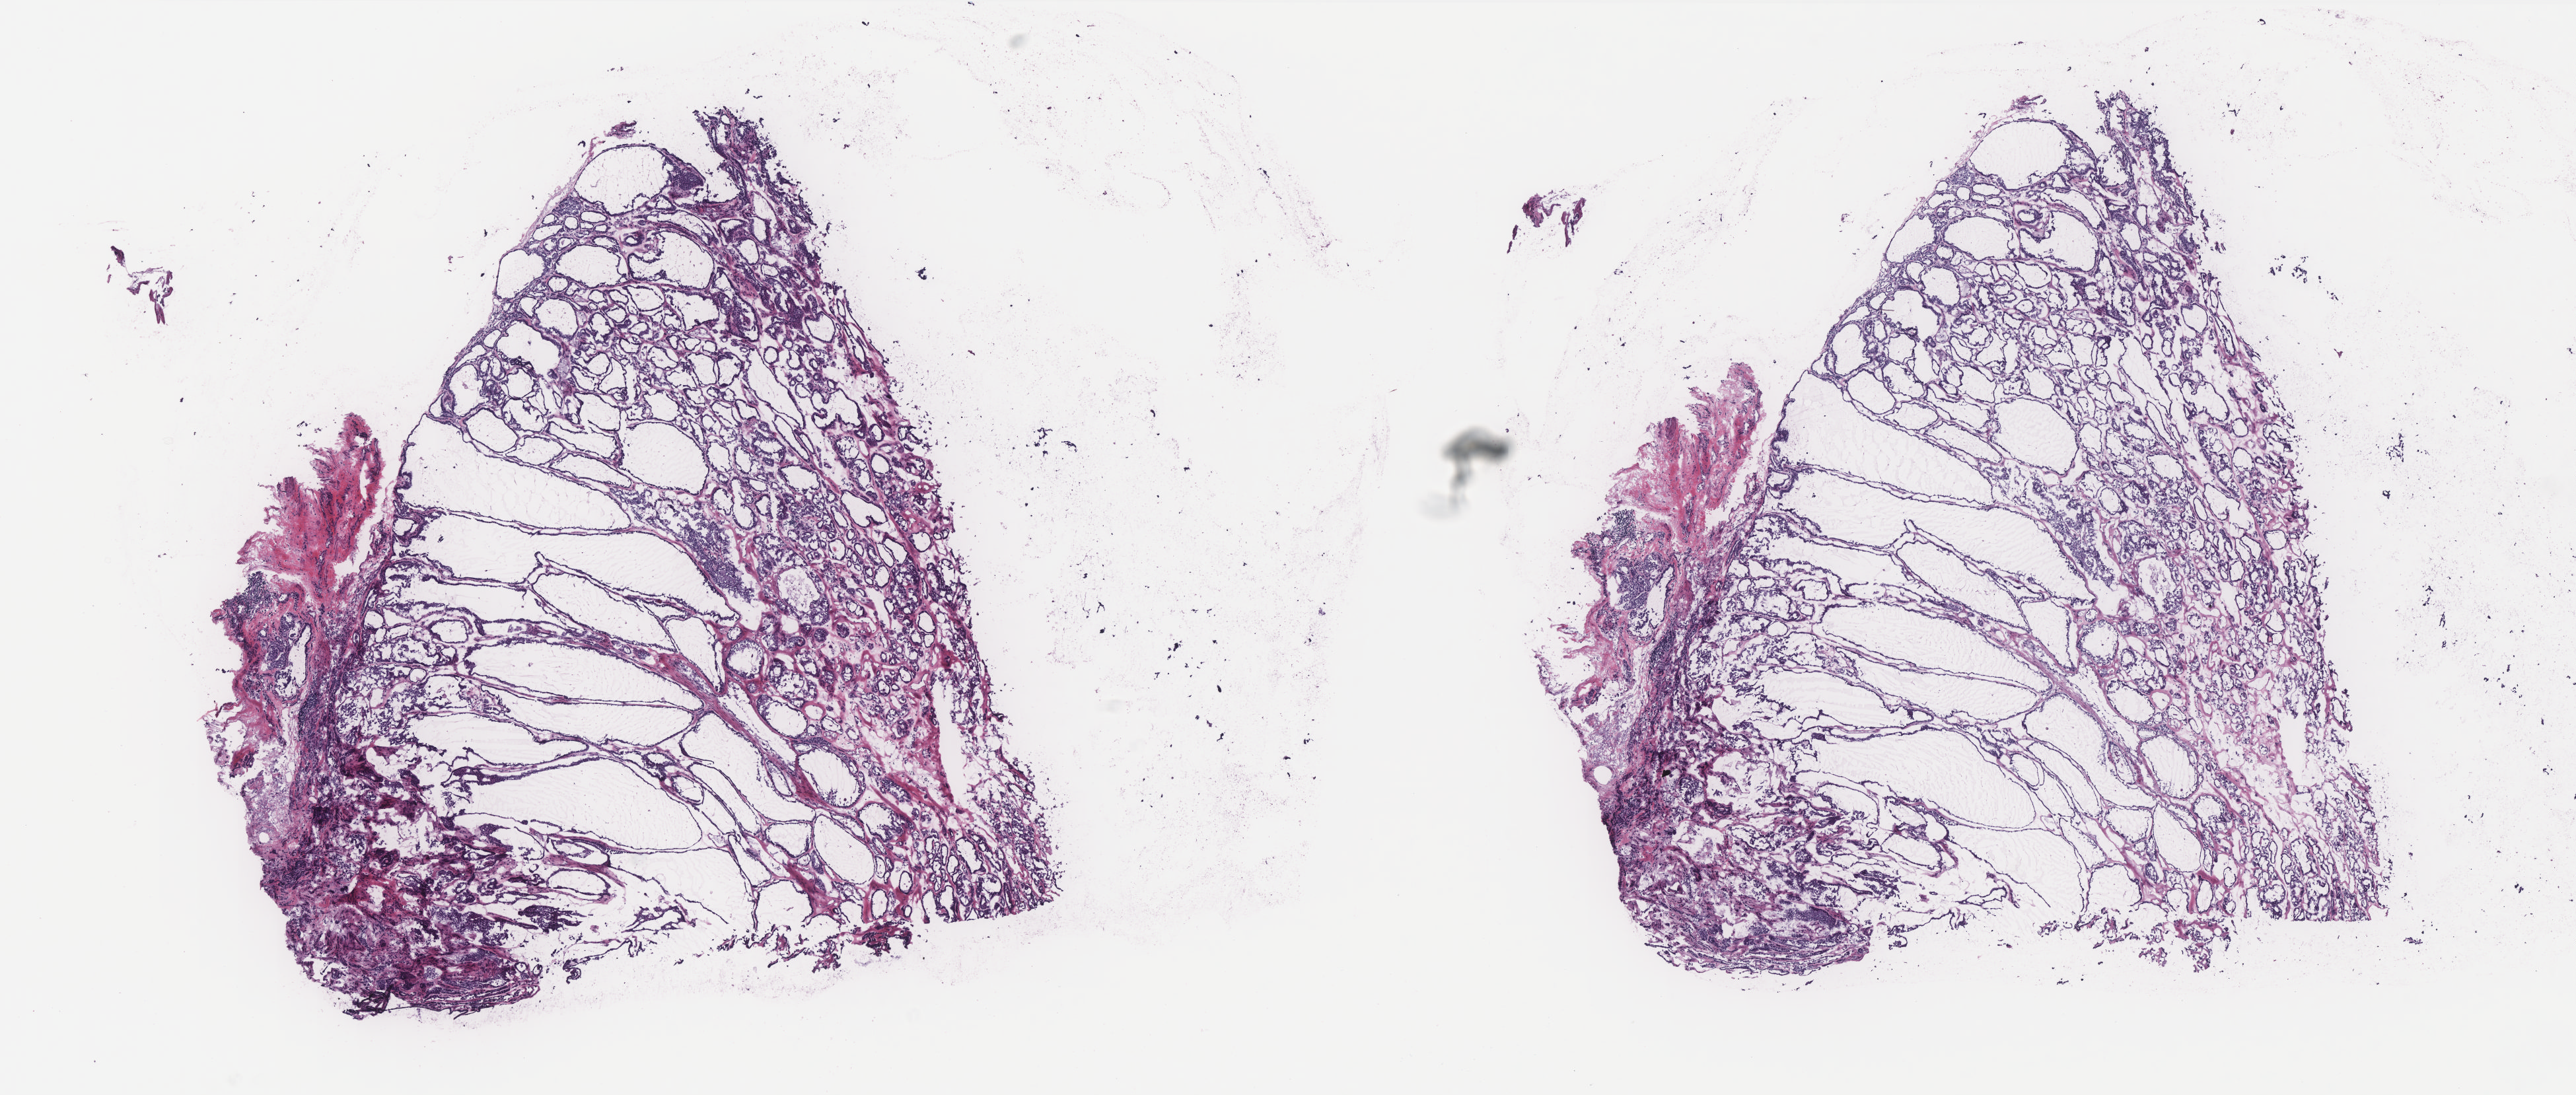
Digitized Hematoxylin and eosin (H&E) stained tissue section (whole slide) — a low-resolution overview of the entire scanned area, about 15.6 x 6.6 mm (acquisition: 40x scan). Frozen section from the bottom of the tissue portion. Primary tumour sample from the thyroid. Patient: male, age at initial diagnosis 55 years. Pathologist review of this section (percent, as recorded): tumour cells 95%, tumour nuclei 80%, normal cells 0%, stromal cells 5%, necrosis 0%. Inflammatory infiltration, as recorded: lymphocyte infiltration 0%, monocyte infiltration 0%, neutrophil infiltration 0%.
- pathologic diagnosis: Papillary adenocarcinoma, NOS
- AJCC pathologic stage: I
- TNM: T1 N0 M0
- laterality: bilateral